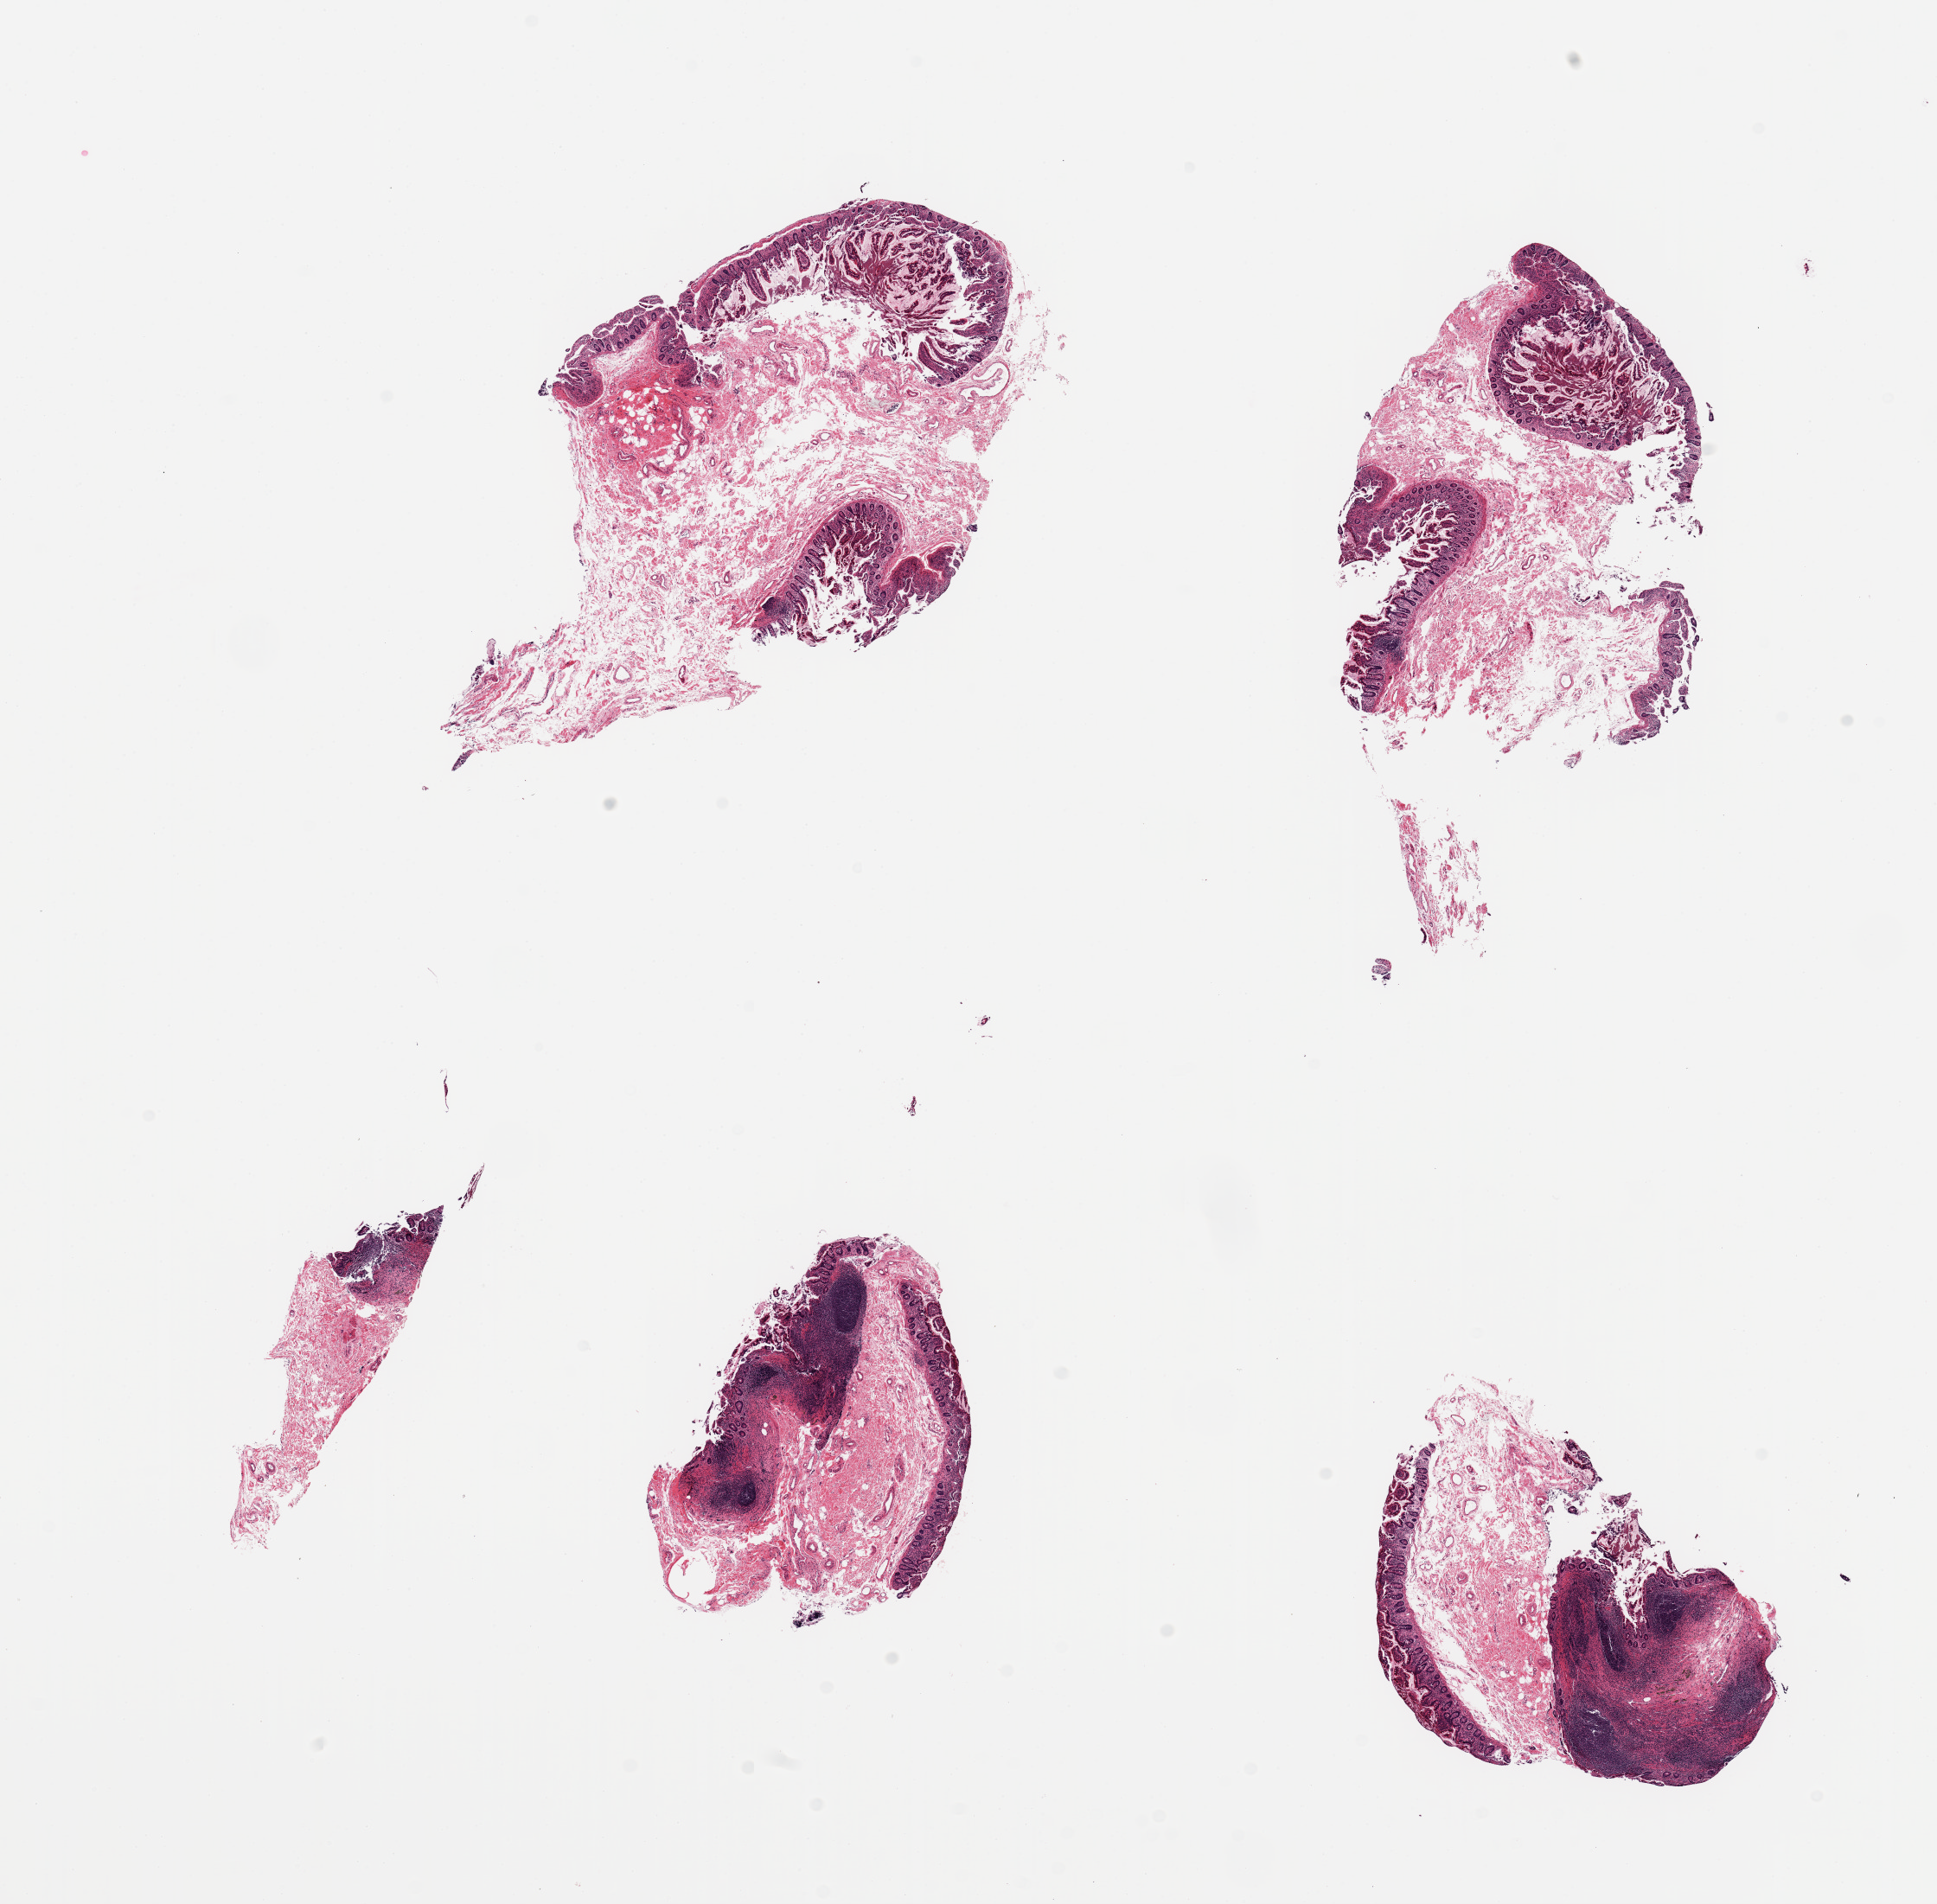
Haematoxylin and eosin whole-slide image — whole scanned area (about 17.7 x 17.4 mm, acquisition: 20x scan) shown as a low-resolution overview; PAXgene-fixed, paraffin-embedded tissue; sampled site (target tissue): ileum; donor tissue sample. Female donor.
- reviewer comment on this tissue sample: 4 pieces, lymphoid aggregates ~10-15% total